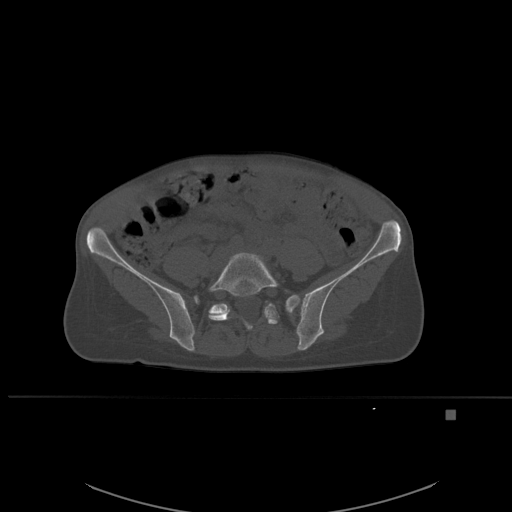
CT including the spine, one axial slice; slice 169 of 537 in the series (ordered by position); bone window (W 1800 / L 400 HU); 512 × 512 image matrix, field of view 440 × 440 mm. Patient: female, 45 years. From the clinical record (not read from this slice): primary cancer: lung.
Annotated regions visible in this slice (semi-automatic segmentation, software-assisted and operator-edited):
- L5 vertebra: bounding box <208,252,300,330> (left, top, right, bottom; pixels)